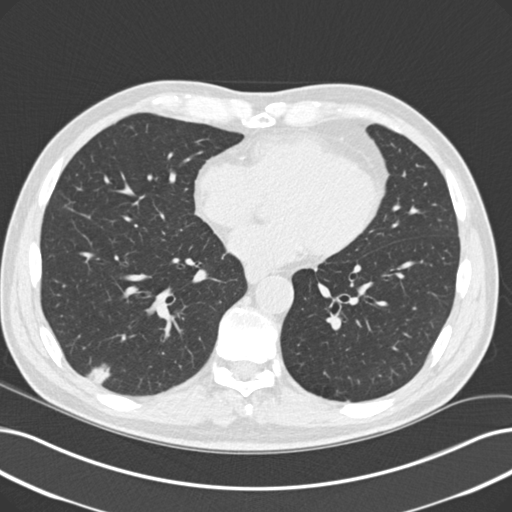
Chest CT (low-dose screening protocol), one axial image, first (baseline) screen, lung window (W 1500 / L -600 HU), 120 kVp, 512 × 512 image matrix. Male, age 60 years at enrolment.
Expert-annotated lung lesion, bounding box (x1, y1, x2, y2) in pixels: (75, 357, 119, 402). The screening reader recorded 2 non-calcified nodules or masses ≥4 mm on this exam; which of them this box marks is not recorded.